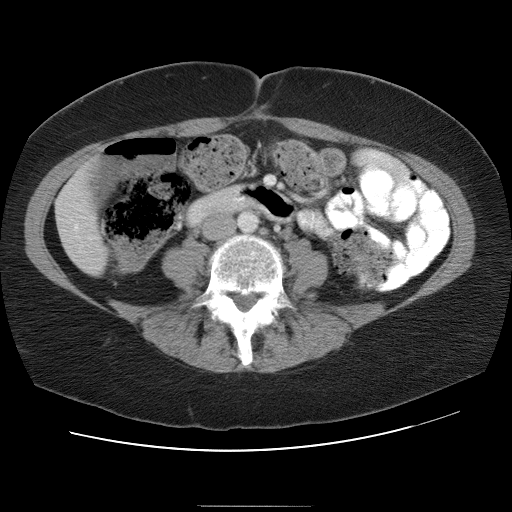
Contrast-enhanced abdominal CT, one axial slice. Position 5 of 30 along the scan axis. 120 kVp. Intravenous contrast given. Soft-tissue window (W 400 / L 40 HU). 512 × 512 image matrix, field of view 376 × 376 mm. Female patient, age 52 years. From the clinical record (not read from this slice): diagnosis: colorectal cancer liver metastases, imaged before liver resection; multiple liver metastases: no.
Structures marked on this image (manually delineated by an expert):
- hepatic veins: bounding box <74,226,77,229> (left, top, right, bottom; pixels)
- liver: <55,161,108,275>